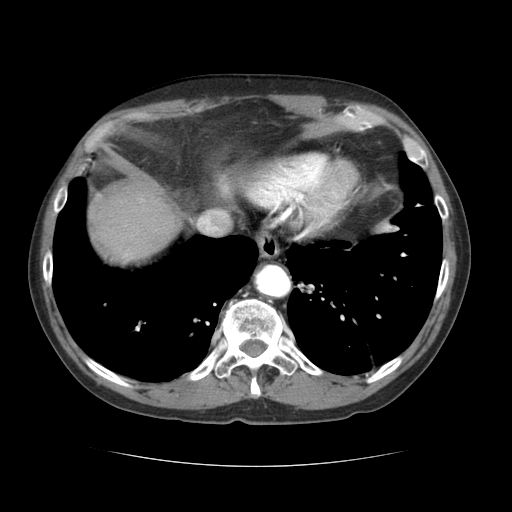
Contrast-enhanced abdominal CT (liver protocol), one axial slice; position 58 of 69 along the scan axis; soft-tissue window (W 400 / L 40 HU); 2.5 mm slice thickness; 512 × 512 image matrix, field of view 360 × 360 mm. Case-level facts recorded for this patient, not image findings: diagnosis: hepatocellular carcinoma (patient treated with transarterial chemoembolisation; whether this scan precedes or follows treatment is not stated here); TNM stage (as recorded): Stage-II; Child-Pugh class: B; tumour differentiation: poorly differentiated; tumour nodularity: multinodular.
Structures marked on this image (semi-automatic segmentation, software-assisted and operator-edited):
- abdominal aorta: box from (x=257, y=266) to (x=289, y=295) px
- liver parenchyma outside the tumour (the mass and vessels are separate outlines, so this box may not span the whole liver): (x=88, y=186)–(x=181, y=262)